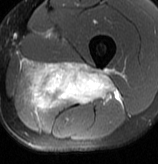
MRI of an extremity soft-tissue mass, one axial slice; slice 41 of 70 in the series (ordered by position); T2-weighted fat-saturated; MR volume resampled by the dataset authors to the PET/CT grid (not the native acquisition matrix); 3.27 mm slice thickness; 158 × 164 image matrix, field of view 154 × 160 mm. Male patient. From the clinical record (not read from this slice): histological type: extraskeletal osteosarcoma; grade: high; site of the primary tumour: left adductur.
Outlined on this slice (expert contour drawn on MRI and transferred to this co-registered scan by the dataset authors):
- gross tumour volume (mass): box from (x=20, y=59) to (x=121, y=109) px